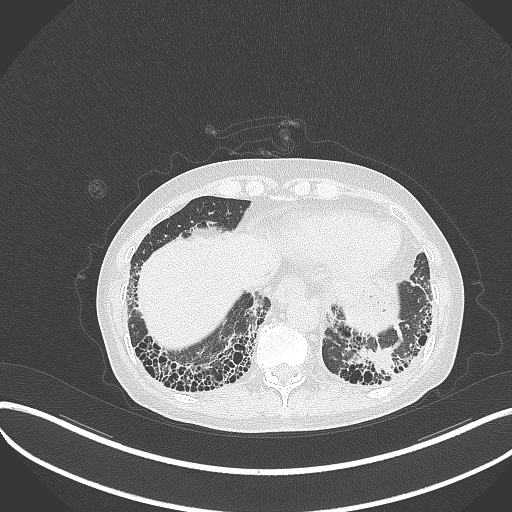
Chest CT, one axial slice; lung window (W 1500 / L -600 HU); 512 × 512 image matrix. Female patient, age 56 years. From the clinical record (not read from this slice): clinical TNM (as recorded): T1 N0 M0.
Outlined on this slice (rectangle marked by the reading radiologist):
- lung tumour (recorded histology: adenocarcinoma): bounding box (x1, y1, x2, y2) in pixels: (355, 344, 398, 378)